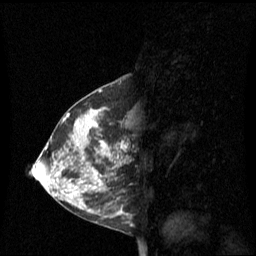
Breast MRI (dynamic contrast-enhanced), one sagittal slice; position 31 of 60 along the scan axis; dynamic contrast-enhanced series, image 2 of 3 at this slice position (ordered by acquisition); 1.5 T; TE 4.2 ms, TR 8.4 ms; 2.1 mm slice thickness; 256 × 256 image matrix, field of view 240 × 240 mm. Patient: female, 42 years. From the clinical record (not read from this slice): setting: breast cancer imaged before/during neoadjuvant chemotherapy; receptor status: HR-positive, HER2-negative.
Structures marked on this image (semi-automatically segmented with operator editing):
- analysis volume of interest (the breast-tissue region the enhancement analysis was run in; not a lesion): box from (x=68, y=110) to (x=129, y=201) px
- tumour enhancement mask (voxels above the 70 % enhancement threshold inside the analysis volume of interest): (x=86, y=112)–(x=127, y=159)